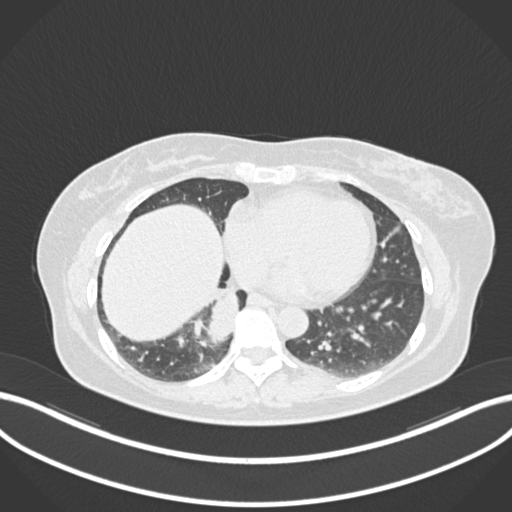
Chest CT, one axial slice. Position 549 of 677 along the scan axis. Reconstruction kernel B30f. Lung window (W 1500 / L -600 HU). 512 × 512 image matrix. Female patient, age 54 years. From the clinical record (not read from this slice): clinical TNM (as recorded): T4 N0 M0.
Structures marked on this image (bounding box drawn by a radiologist):
- lung tumour (recorded histology: adenocarcinoma): box from (x=207, y=286) to (x=248, y=345) px